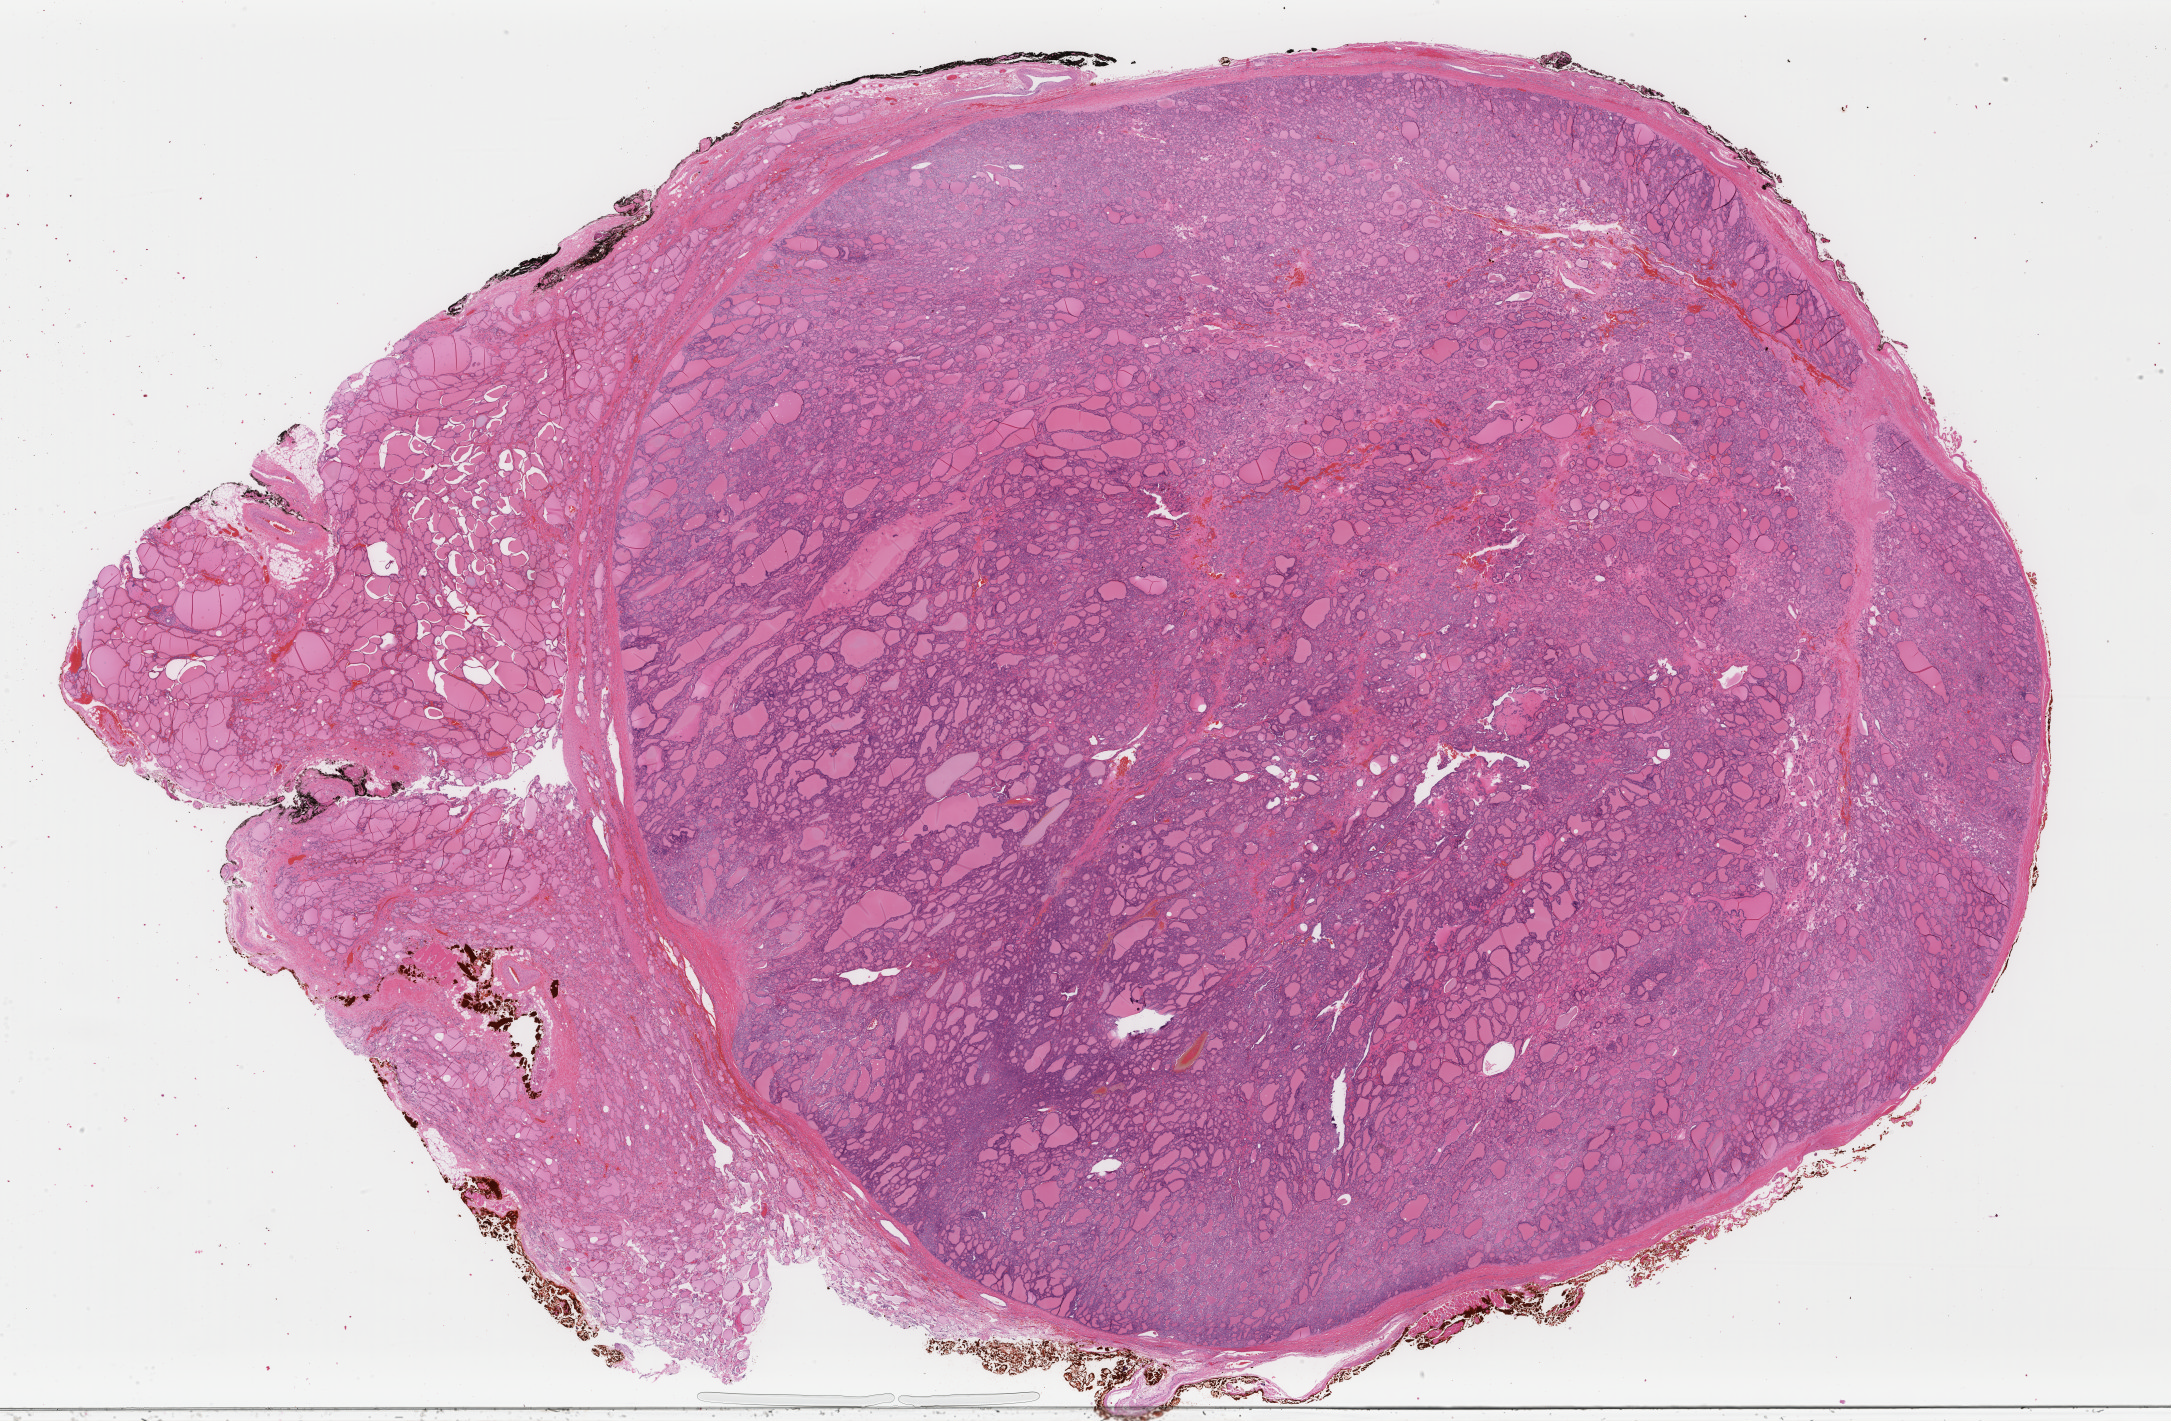
Digitized H&E-stained tissue section (whole slide), low-resolution overview of the scanned area, about 34.5 x 22.6 mm (from a 40x scan). FFPE section. Sample: primary tumour, thyroid. Female, age 34 years at initial diagnosis.
- histologic diagnosis: Papillary carcinoma, follicular variant (thyroid gland)
- laterality: left
- AJCC pathologic stage: I (6th edition)